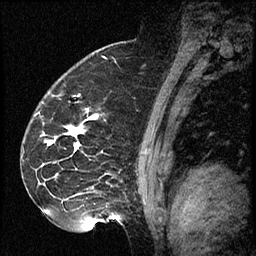
Breast MRI (dynamic contrast-enhanced), one sagittal slice; slice 46 of 60 in the series (ordered by position); dynamic contrast-enhanced series, image 2 of 2 at this slice position (ordered by acquisition); 1.5 T; TE 4.2 ms, TR 17.3 ms; 256 × 256 image matrix, field of view 200 × 200 mm. Female patient. Case-level facts recorded for this patient, not image findings: setting: breast cancer imaged before/during neoadjuvant chemotherapy; receptor status: HR-positive, HER2-negative.
Annotated regions visible in this slice (semi-automatically segmented with operator editing):
- analysis volume of interest (the breast-tissue region the enhancement analysis was run in; not a lesion): box from (x=41, y=95) to (x=115, y=223) px
- tumour enhancement mask (voxels above the 100 % enhancement threshold inside the analysis volume of interest): (x=68, y=128)–(x=79, y=151)